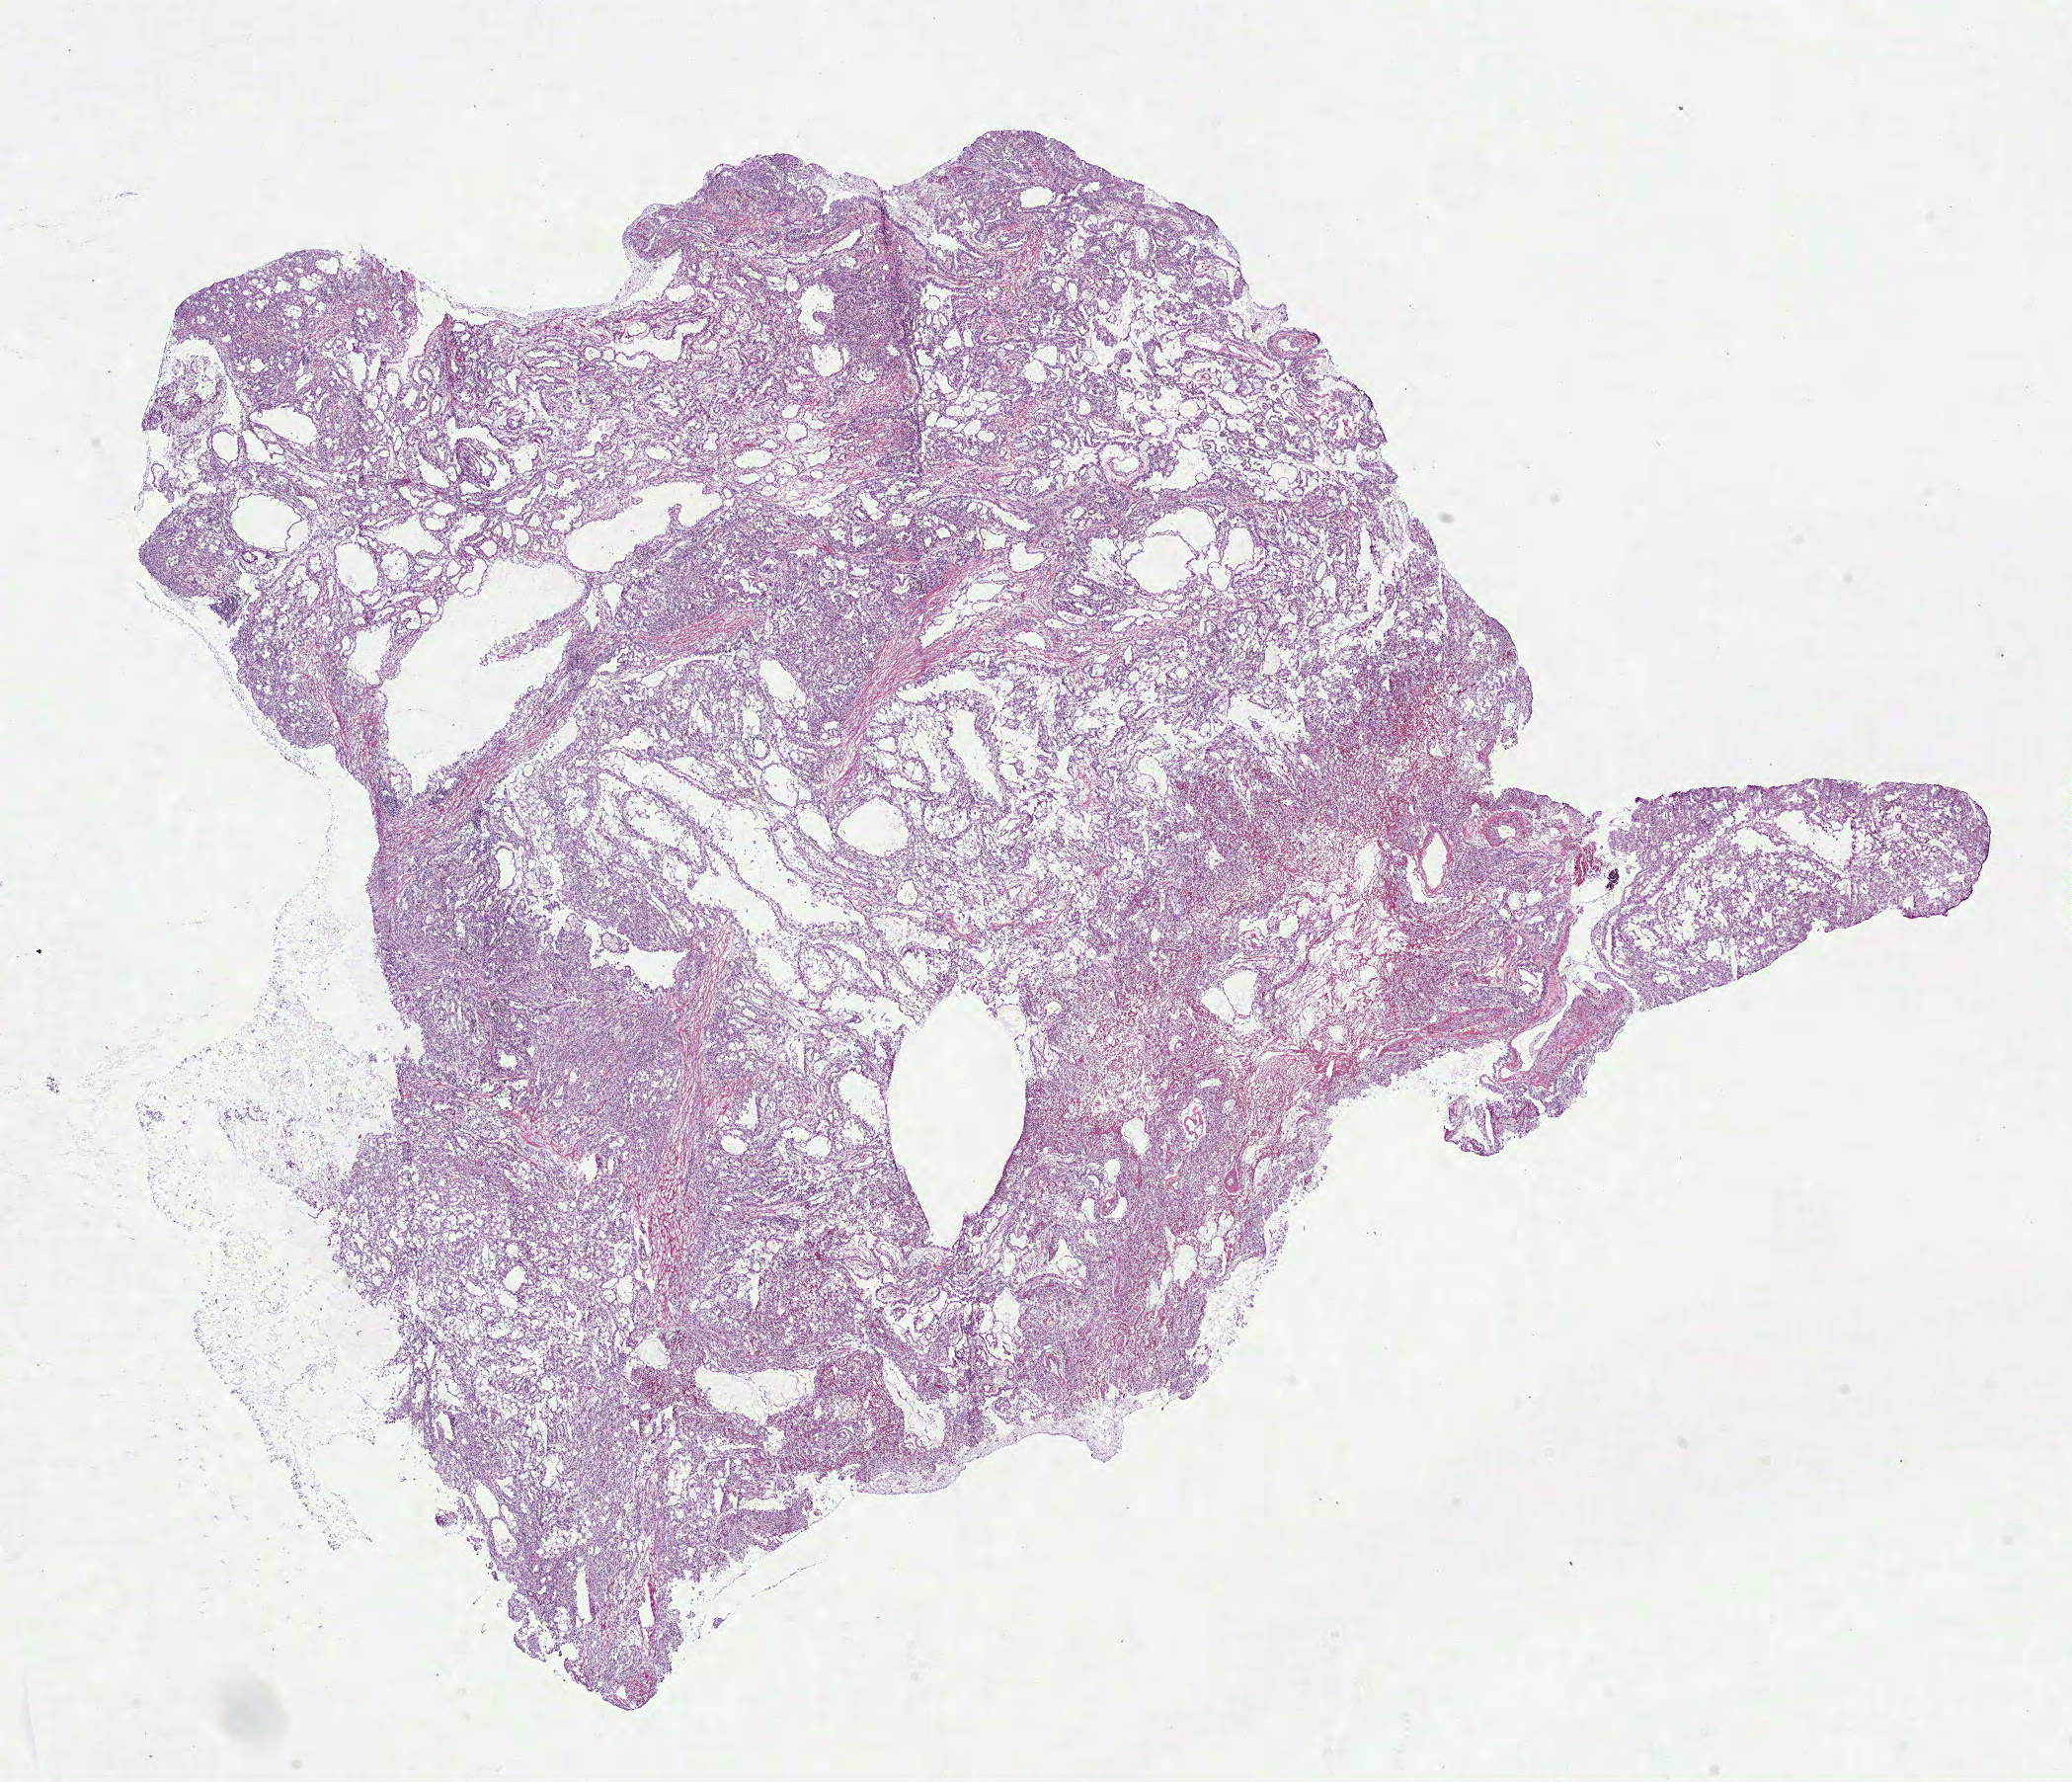
H&E whole-slide image — shown as a low-resolution overview of the whole scanned area (about 16.9 x 14.5 mm, acquisition: 40x scan). Frozen section from the bottom of the tissue portion. Kidney, primary tumour sample. Patient: female, age at initial diagnosis 32 years. Composition of this section per pathologist review: tumour cells 88%, tumour nuclei 80%, normal cells 0%, stromal cells 10%, necrosis 2%.
AJCC pathologic stage: III. Lymph nodes positive (case pathology): 3 of 26 examined. Pathologic diagnosis: Papillary adenocarcinoma, NOS.